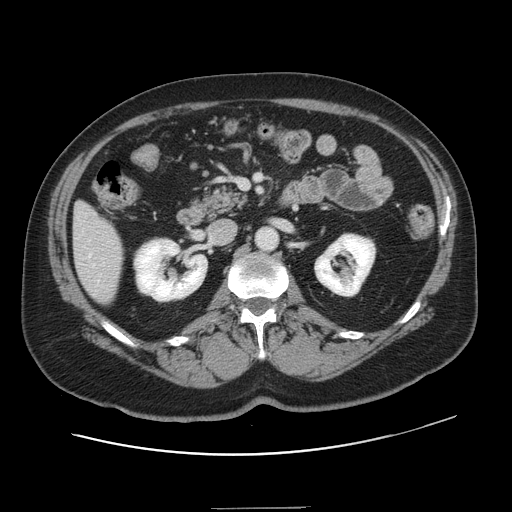
Contrast-enhanced abdominal CT, one axial slice; slice 58 of 143 in the series (ordered by position); 120 kVp; intravenous contrast given; soft-tissue window (W 400 / L 40 HU); 2.5 mm slice thickness; 512 × 512 image matrix, field of view 402 × 402 mm. Male patient, age 62 years. Case-level facts recorded for this patient, not image findings: diagnosis: colorectal cancer liver metastases, imaged before liver resection; multiple liver metastases: yes; largest metastasis: 2.7 cm; disease in both lobes: no.
Structures marked on this image (manually delineated by an expert):
- hepatic veins: bounding box <89,254,95,267> (left, top, right, bottom; pixels)
- liver: <74,203,123,304>